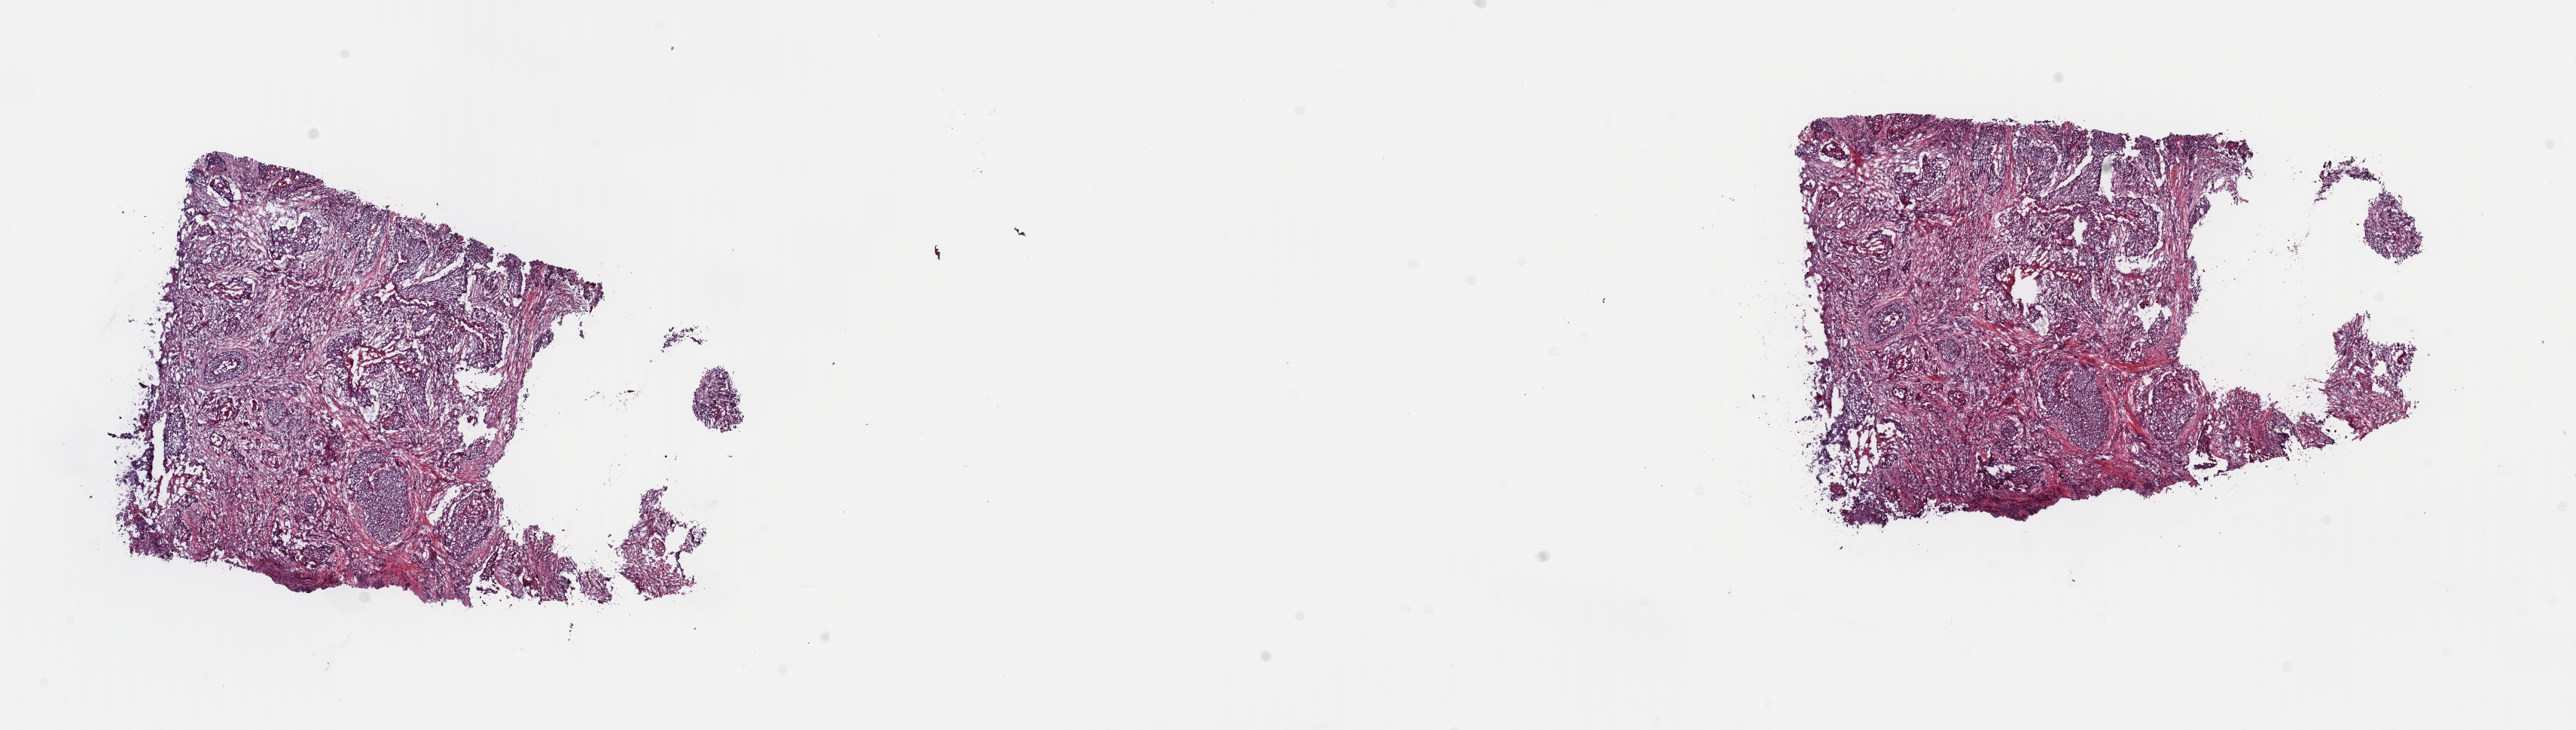
Hematoxylin and eosin (H&E) stained whole-slide image — low-resolution overview of the scanned area, about 27.0 x 7.6 mm (from a 40x scan), frozen section from the top of the tissue portion, primary tumour sample from the lung. Female, age 75 years at initial diagnosis. Composition of this section per pathologist review: tumour cells 75%, tumour nuclei 75%, normal cells 0%, stromal cells 20%, necrosis 5%. Inflammatory infiltration, as recorded: lymphocyte infiltration 4%, monocyte infiltration 1%, neutrophil infiltration 2%.
• AJCC pathologic stage: II
• histologic diagnosis: Squamous cell carcinoma, NOS (upper lobe, lung)
• TNM: T3 N0 MX